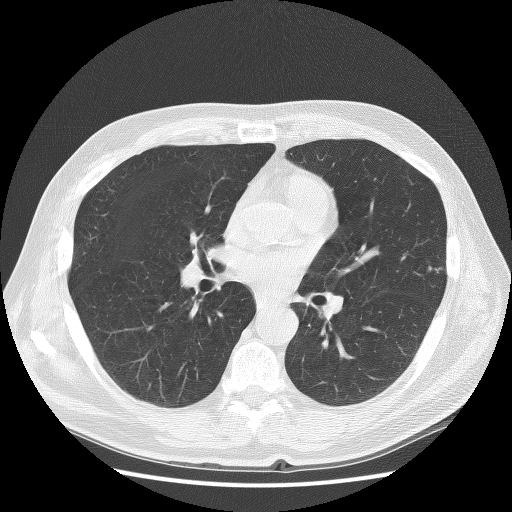
Axial slice from a low-dose chest CT screening exam, baseline annual screen, lung window (W 1500 / L -600 HU), 2.5 mm slice thickness, slice 121 of 272 in the series, 512 × 512 image matrix. Male participant, aged 67 years at enrolment.
Expert-annotated lung lesion, box from (x=406, y=247) to (x=463, y=294) px. No non-calcified nodule or mass ≥4 mm was recorded by the screening reader at this exam. Official screen result: negative screen, minor abnormalities not suspicious for lung cancer. Later outcome: lung cancer diagnosed 772 days after this screen — squamous cell carcinoma, NOS, left upper lobe, moderately differentiated (G2), stage IB (AJCC 6th edition), 25 mm at pathology.